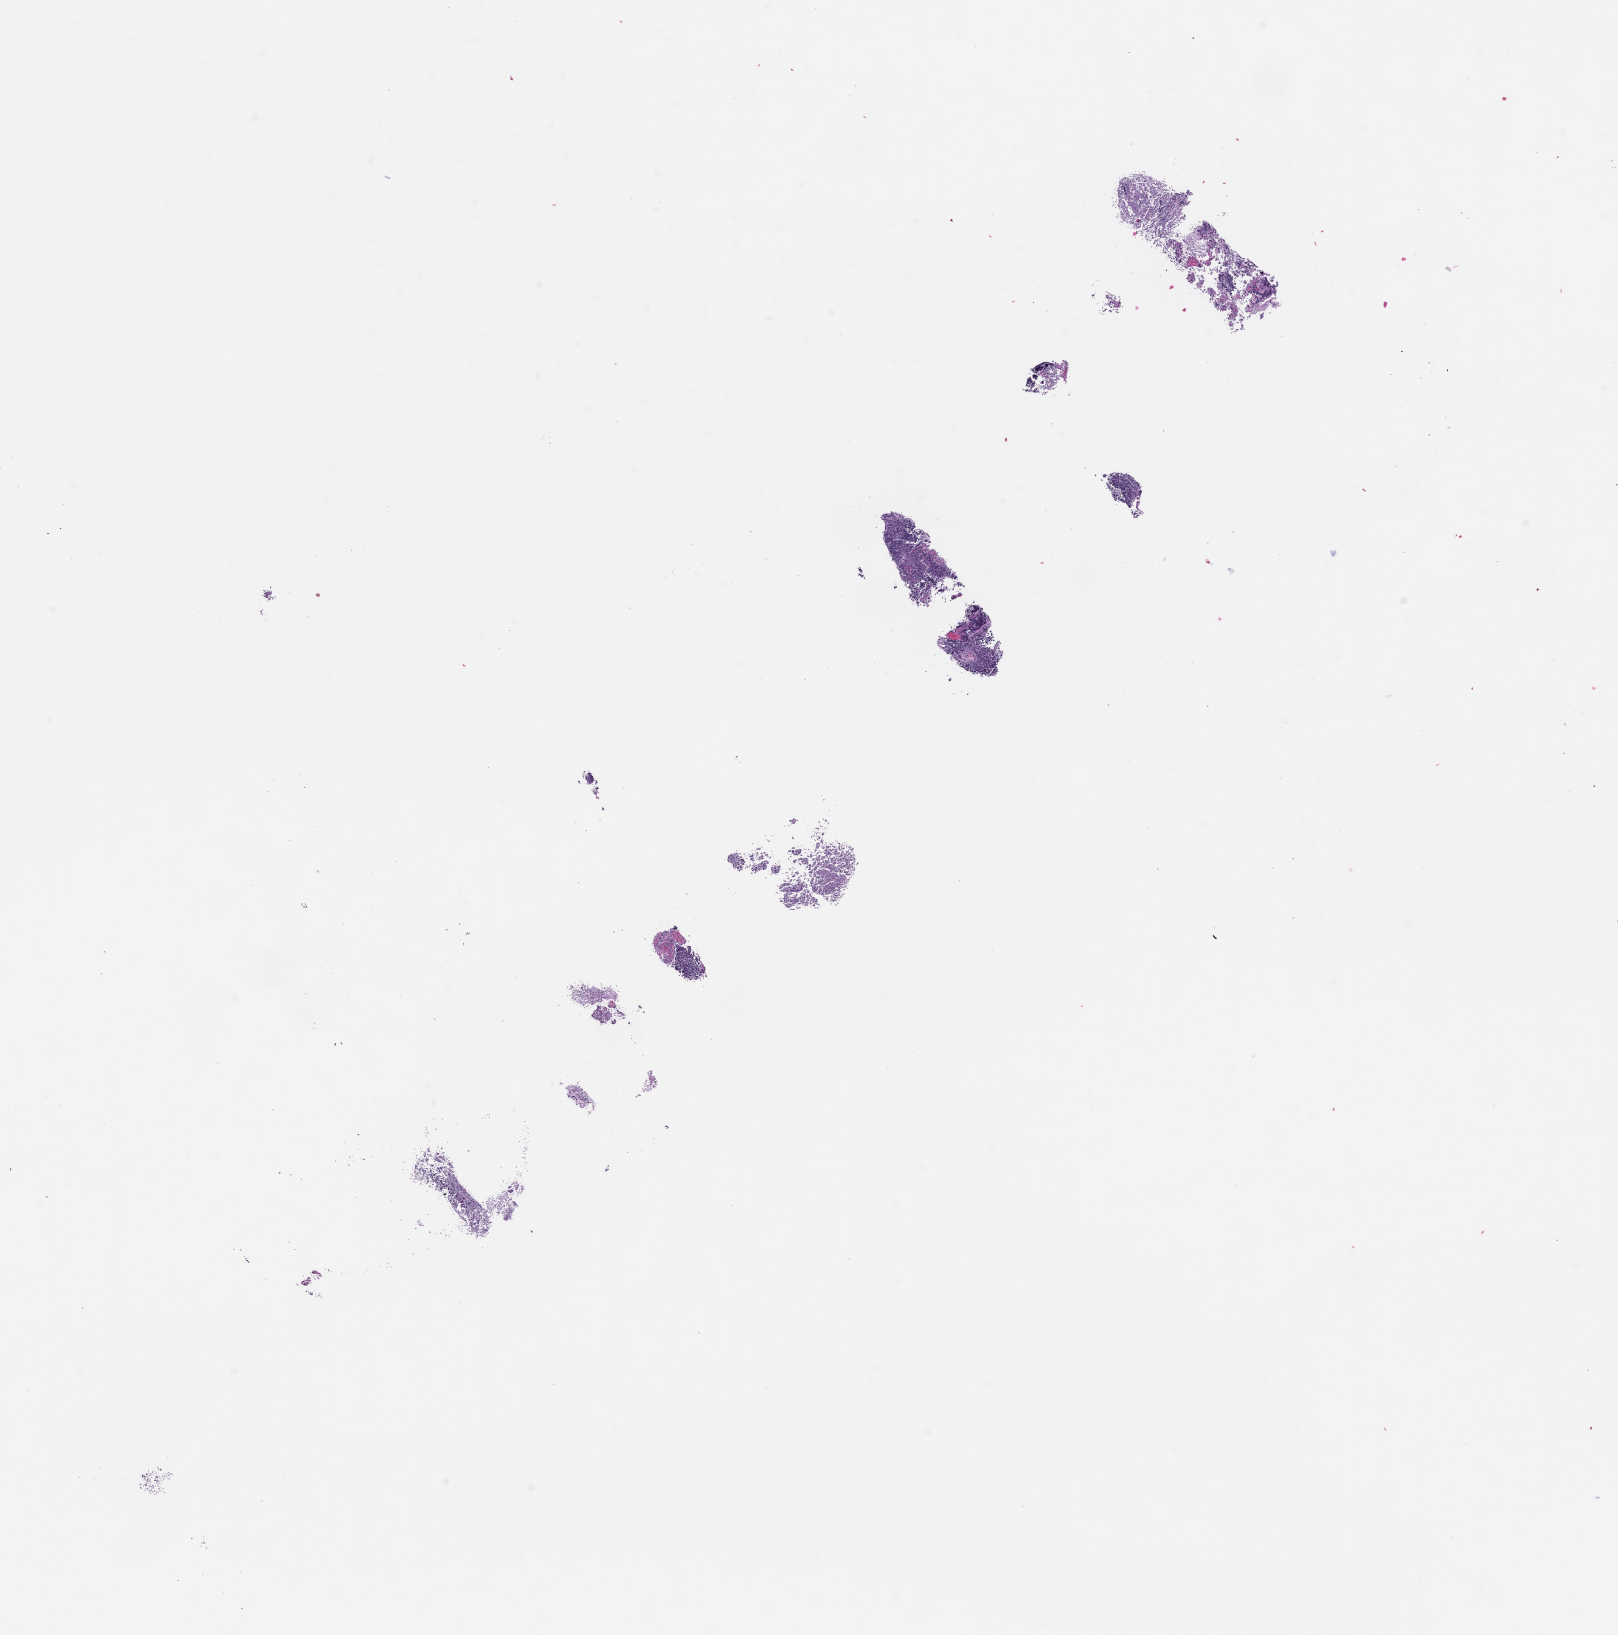
Digitized H&E-stained section — whole scanned area (about 13.1 x 13.2 mm) shown as a low-resolution overview, formalin-fixed, paraffin-embedded (FFPE) tissue, site: lung. Patient sex: female.
This section: primary tumour tissue. Diagnosis: Small Cell Lung Carcinoma.